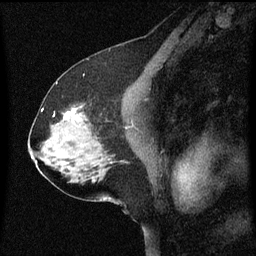
Breast MRI (dynamic contrast-enhanced), one sagittal slice; slice 36 of 60 in the series (ordered by position); dynamic contrast-enhanced series, image 2 of 3 at this slice position (ordered by acquisition); 1.5 T; TE 4.2 ms, TR 8 ms; 2 mm slice thickness; 256 × 256 image matrix, field of view 200 × 200 mm. Female patient, age 58 years.
Annotated regions visible in this slice (semi-automatic segmentation, software-assisted and operator-edited):
- analysis volume of interest (the breast-tissue region the enhancement analysis was run in; not a lesion): bounding box [x1, y1, x2, y2] px = [56, 108, 95, 137]
- tumour enhancement mask (voxels above the 70 % enhancement threshold inside the analysis volume of interest): [66, 110, 81, 121]